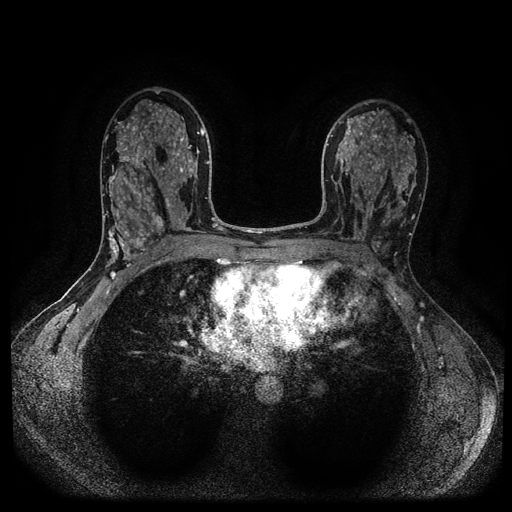
Breast MRI (dynamic contrast-enhanced, multi-phase), one axial slice. Dynamic contrast-enhanced series, time point 2 of 5 at this slice position (early post-contrast). 1.5 T. TE 2.6 ms, TR 5.4 ms. 512 × 512 image matrix. Patient: female, 43 years.
Structures marked on this image (semi-automatic segmentation, software-assisted and operator-edited):
- breast lesion (labelled benign in the annotation): bounding box <149,211,165,234> (left, top, right, bottom; pixels)